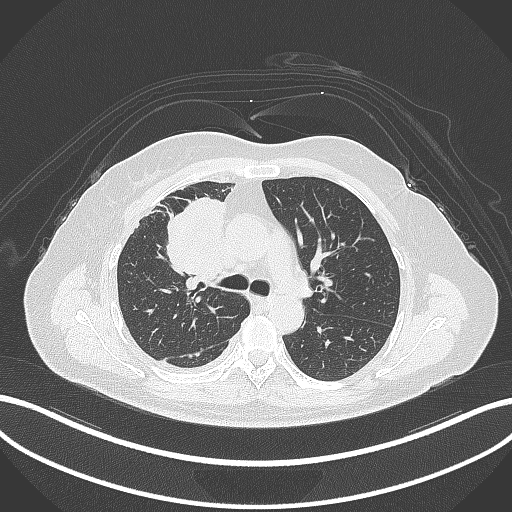
Chest CT, one axial slice; slice 183 of 305 in the series (ordered by position); 120 kVp; lung window (W 1500 / L -600 HU); 1 mm slice thickness; 512 × 512 image matrix. Patient: female, 52 years. From the clinical record (not read from this slice): clinical TNM (as recorded): T3 N1 M1.
Outlined on this slice (bounding box drawn by a radiologist):
- lung tumour (recorded histology: adenocarcinoma): bounding box <155,196,229,284> (left, top, right, bottom; pixels)